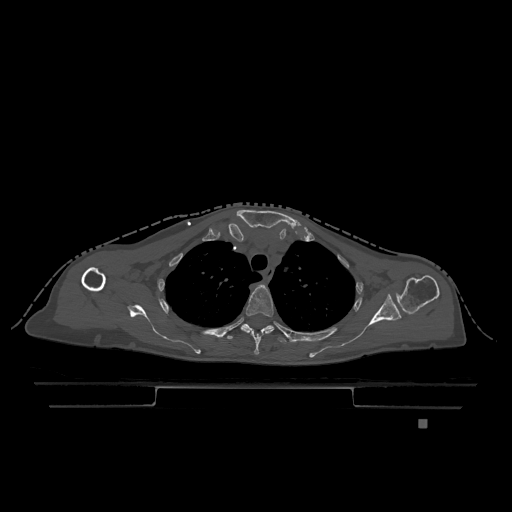
CT including the spine, one axial slice; slice 911 of 1317 in the series (ordered by position); bone window (W 1800 / L 400 HU); 0.5 mm slice thickness; 512 × 512 image matrix, field of view 500 × 500 mm. Female patient, age 74 years. Case-level facts recorded for this patient, not image findings: primary cancer: lung; vertebrae with lytic lesions (as recorded): T1, T4, T5, T6, L4, L5.
Annotated regions visible in this slice (semi-automatically segmented with operator editing):
- T3 vertebra: bounding box [x1, y1, x2, y2] px = [240, 286, 274, 355]
- T4 vertebra: [227, 323, 307, 343]